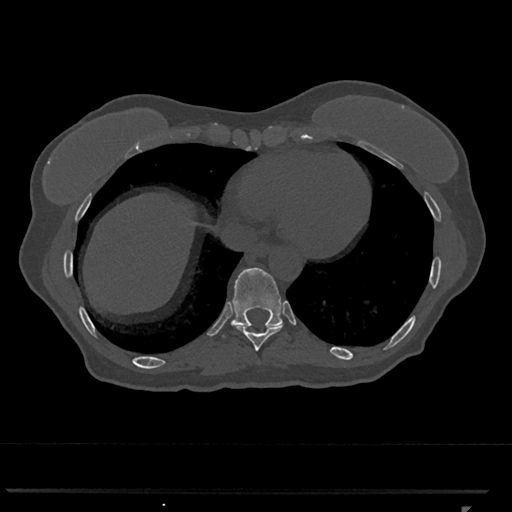
CT including the spine, one axial slice; reconstruction kernel Br40s/3; 120 kVp; bone window (W 1800 / L 400 HU); 0.5 mm slice thickness; 512 × 512 image matrix, field of view 380 × 380 mm. Patient: female, 62 years. From the clinical record (not read from this slice): primary cancer: renal.
Outlined on this slice (semi-automatically segmented with operator editing):
- T10 vertebra: box from (x=222, y=267) to (x=283, y=338) px
- T9 vertebra: (x=233, y=323)–(x=283, y=351)